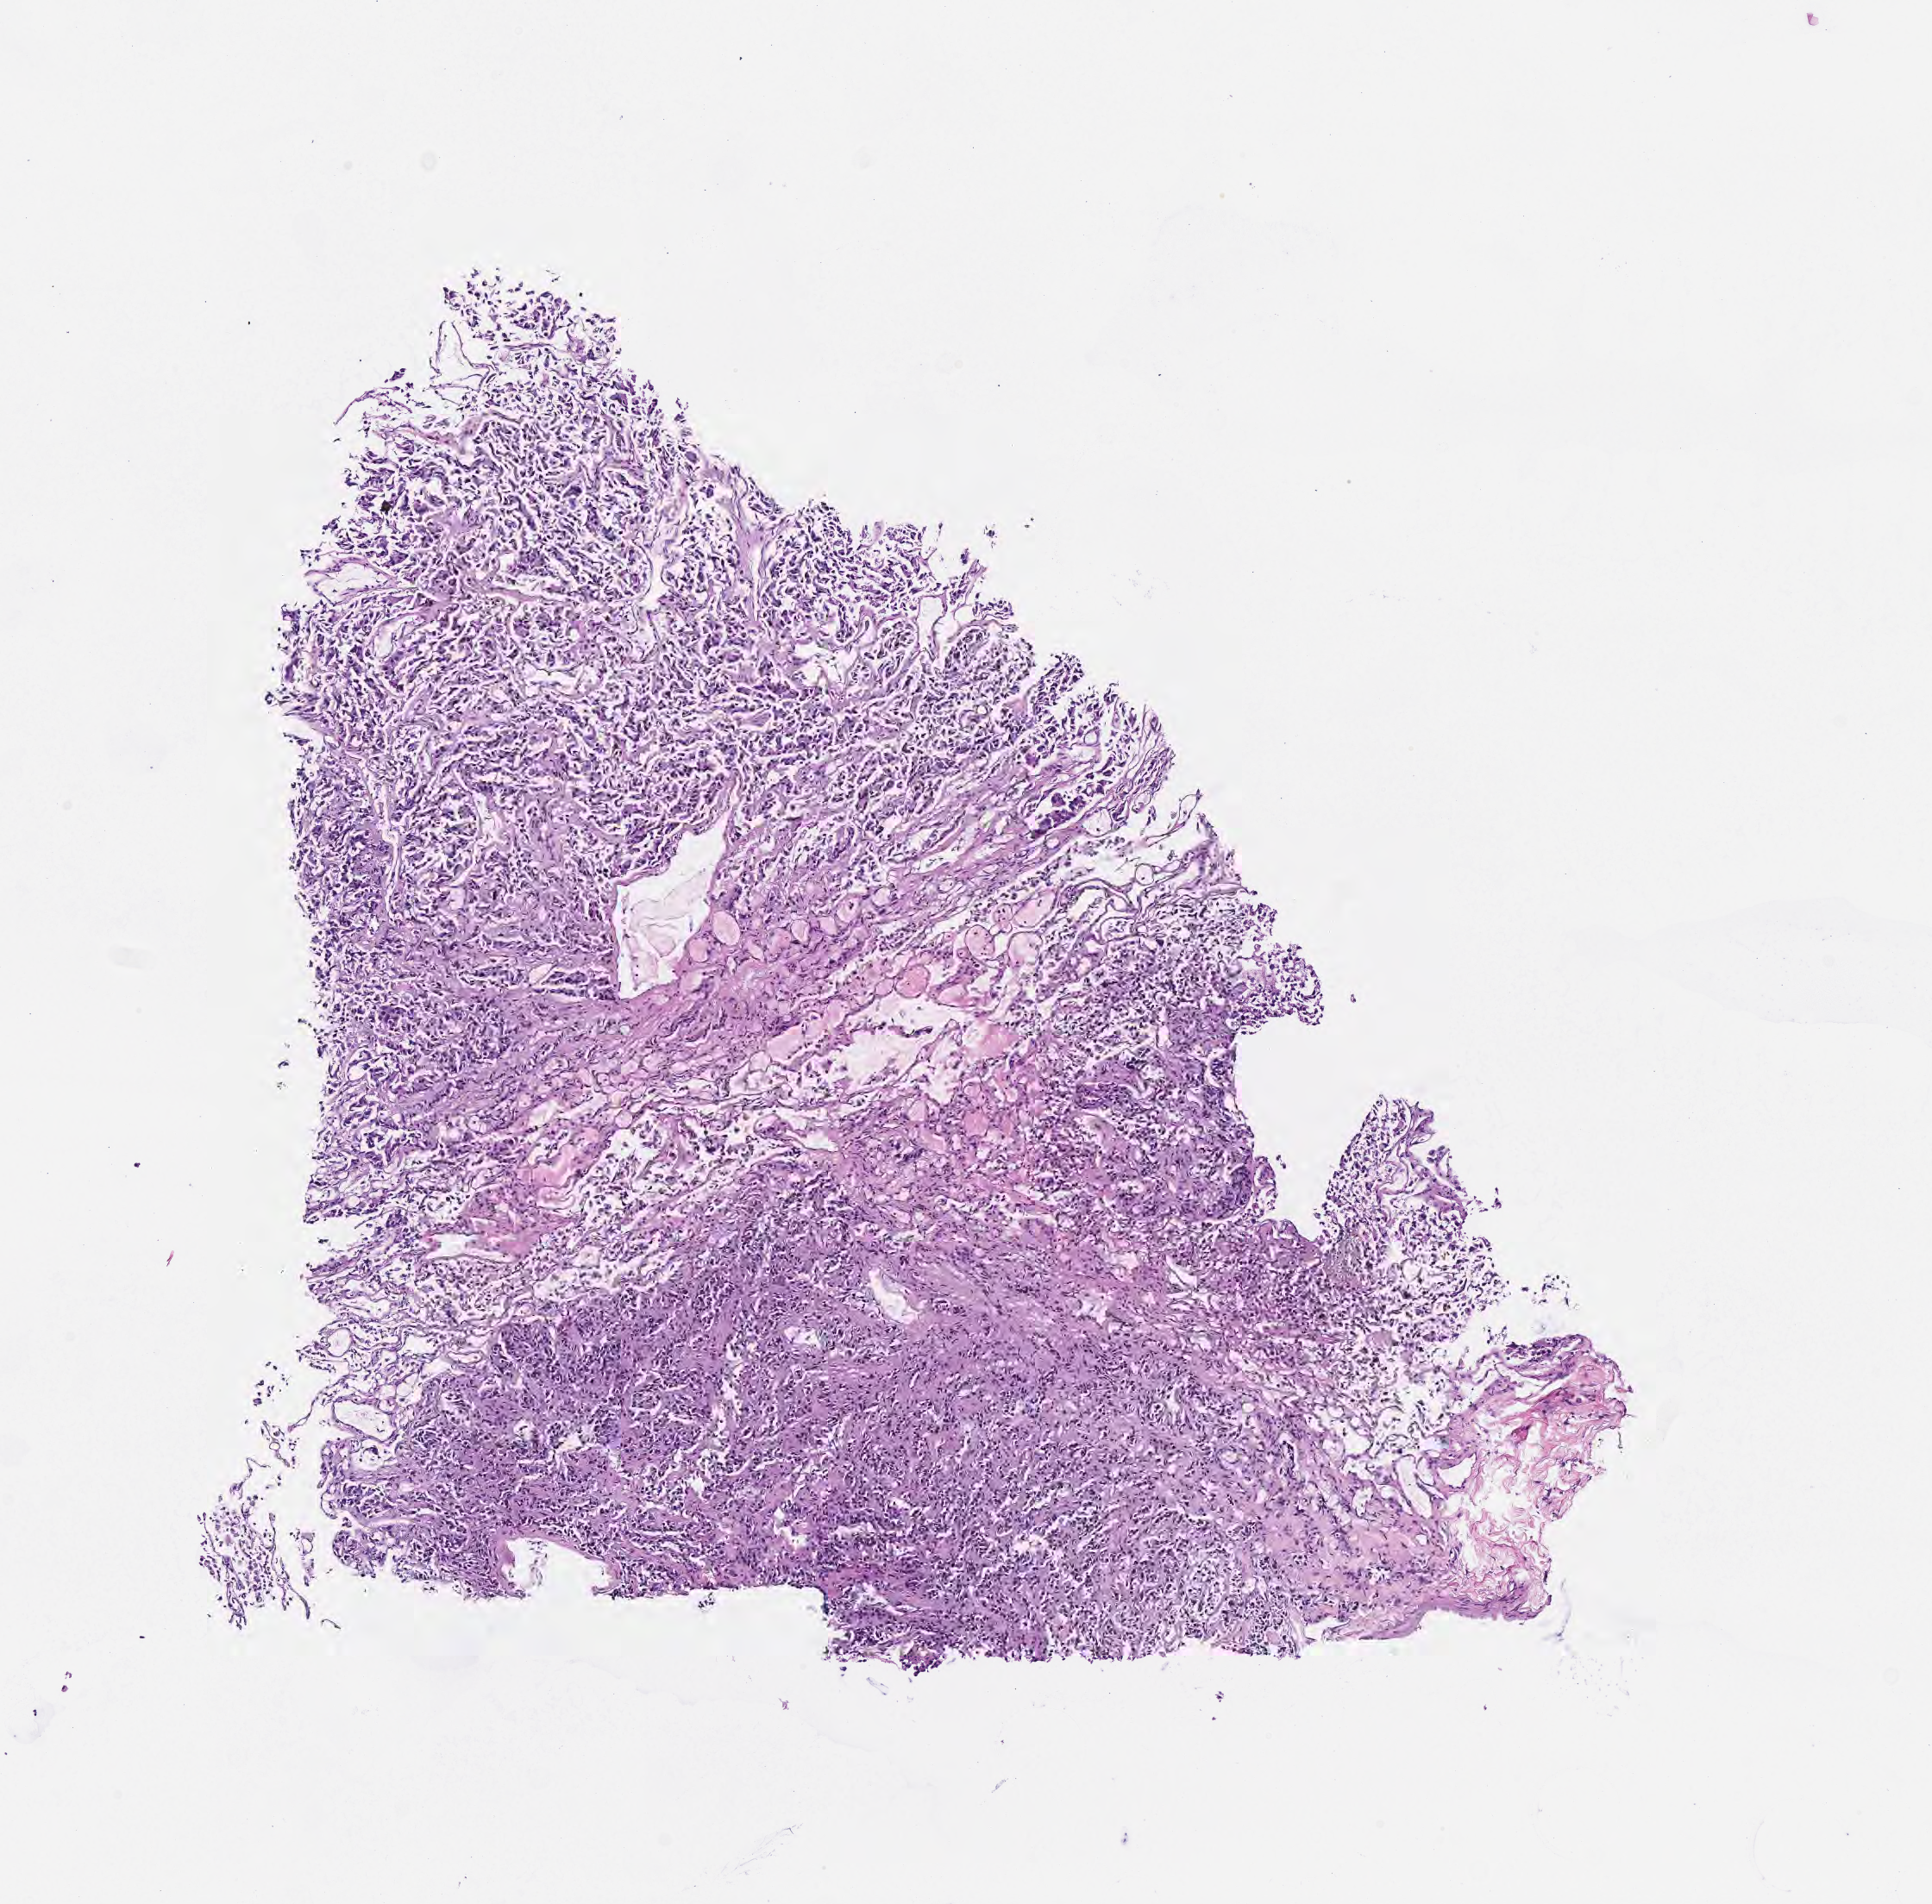
Whole-slide image, hematoxylin and eosin (H&E) stain, shown as a low-resolution overview of the whole scanned area (about 4.5 x 4.5 mm); specimen: tumor tissue. Male patient.
* diagnosis: Neoplasm, uncertain whether benign or malignant